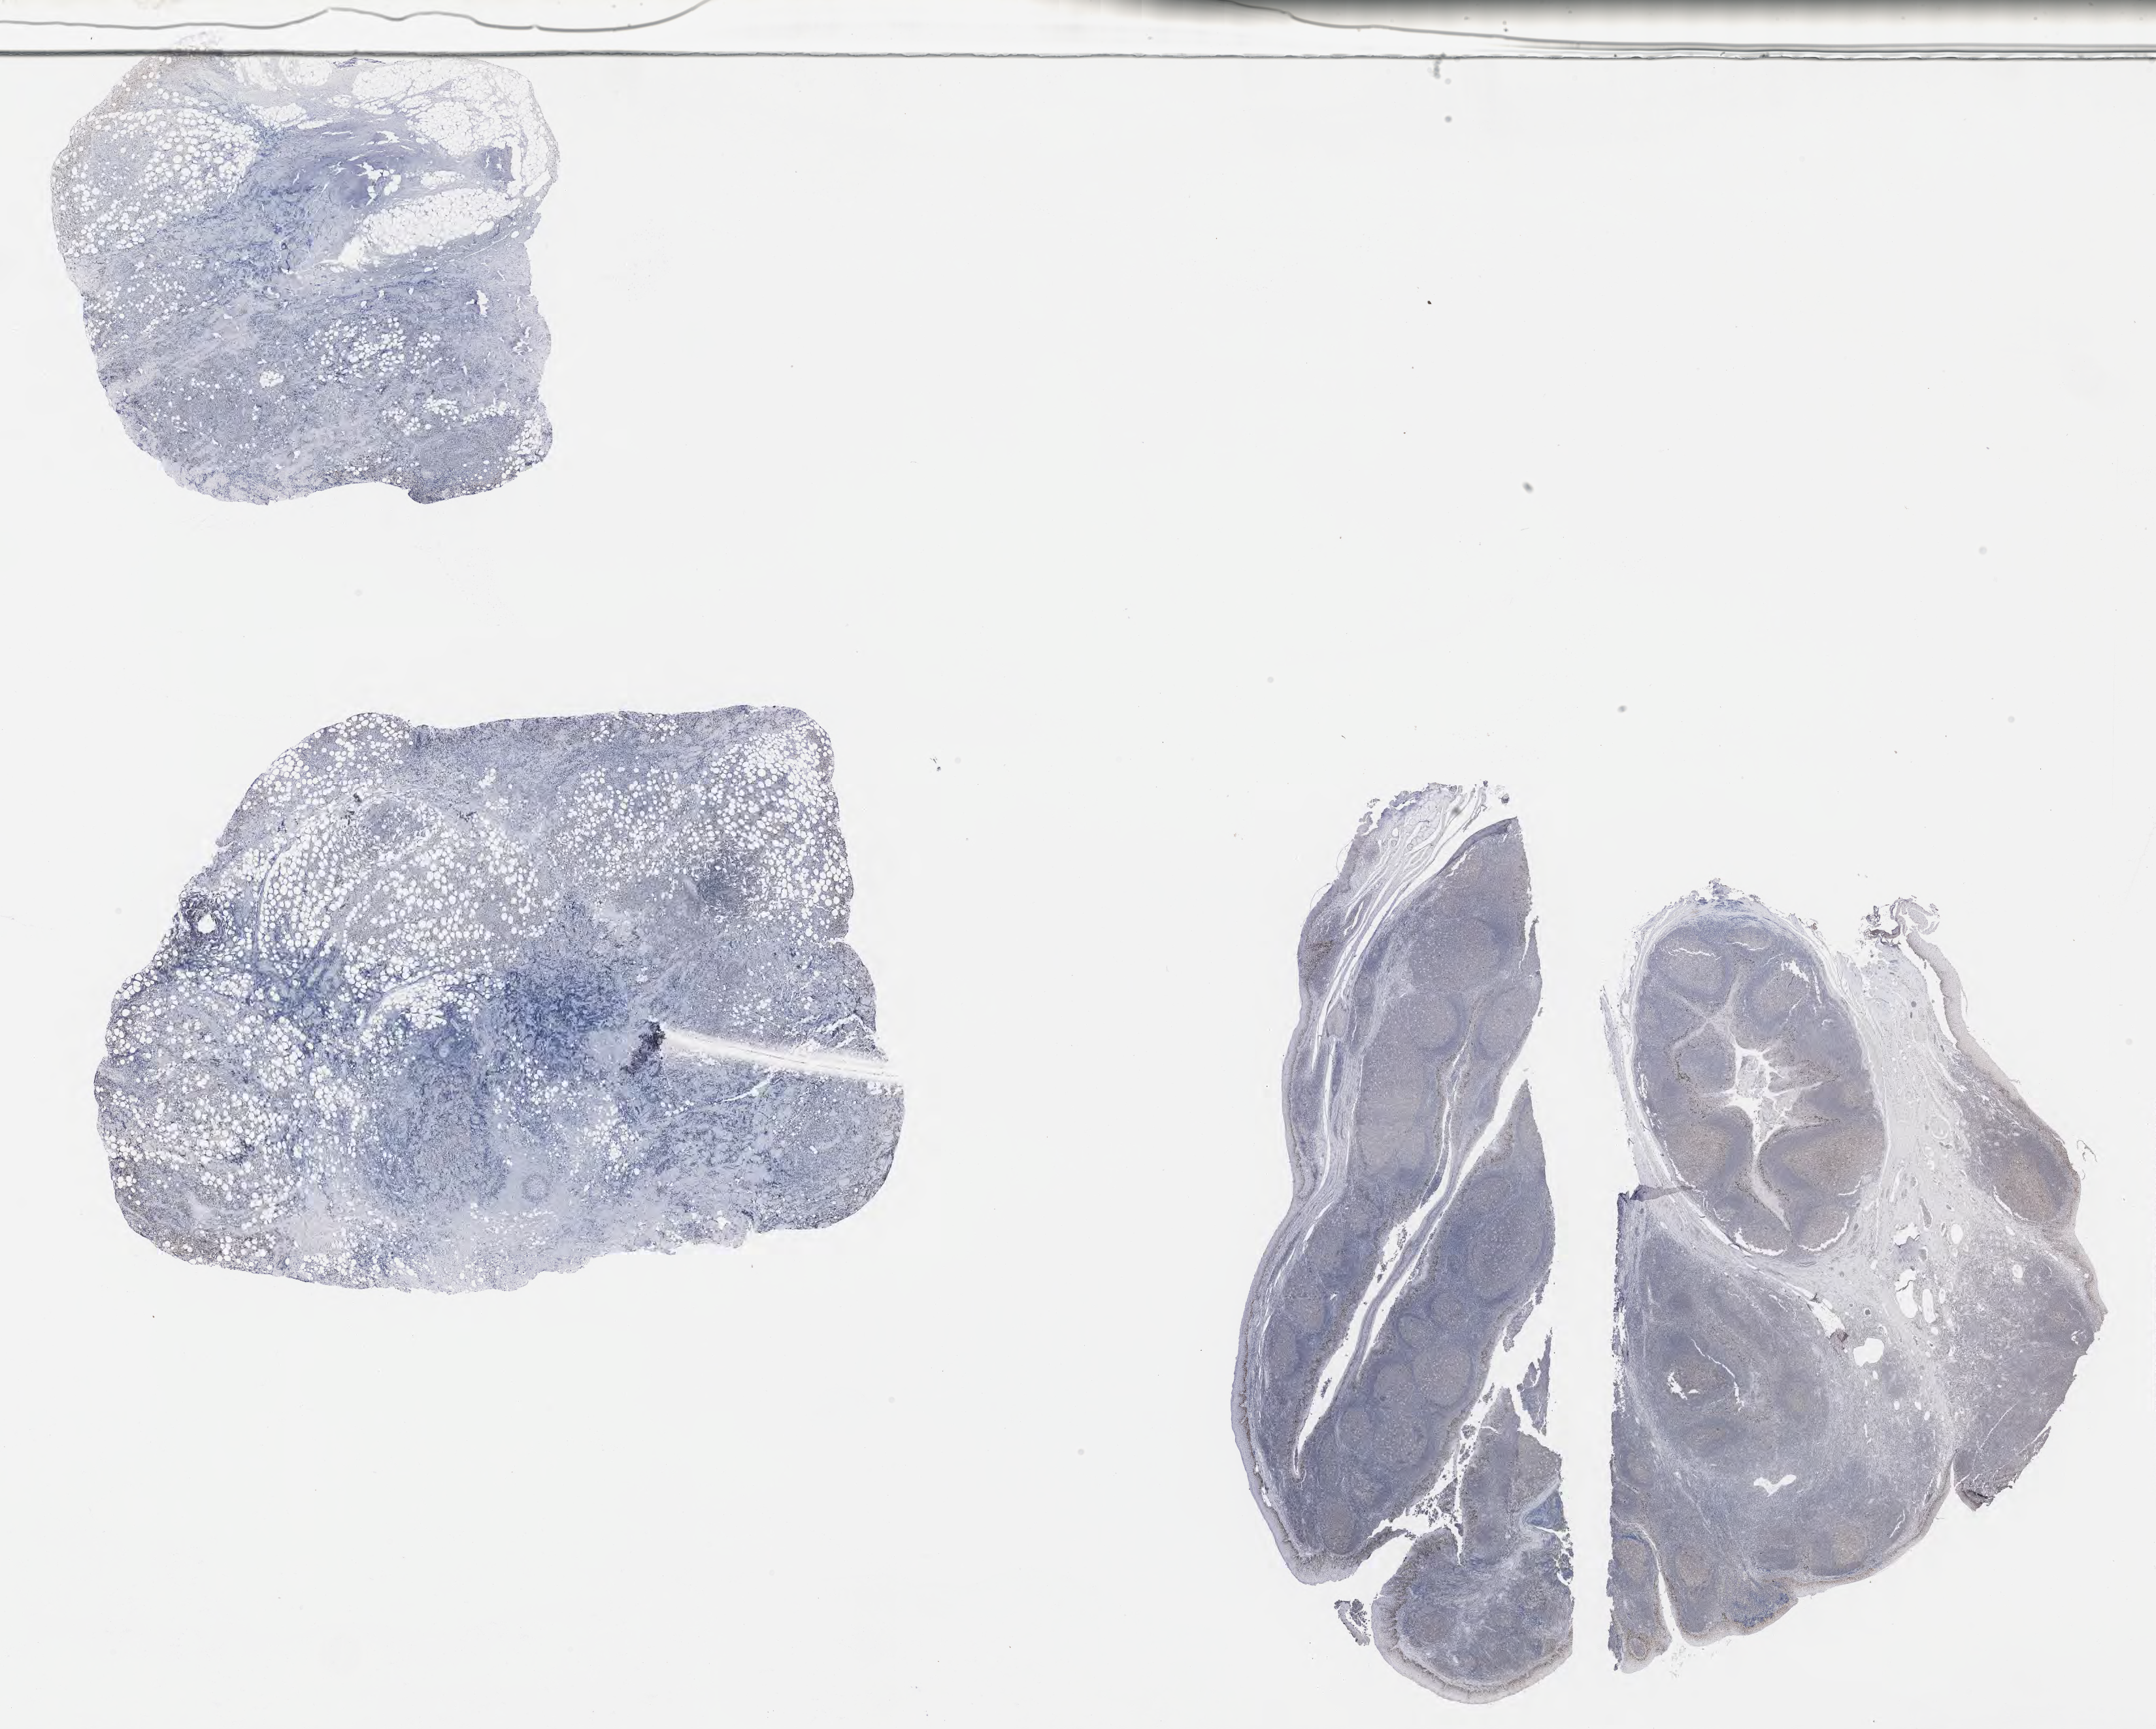
Immunohistochemistry (IHC) whole-slide image stained for p53, a low-resolution overview of the entire scanned area, about 26.7 x 21.4 mm, specimen: tumor tissue, site: kidney. Patient male; aged 63.
Diagnosis: Diffuse large B-cell lymphoma, NOS.